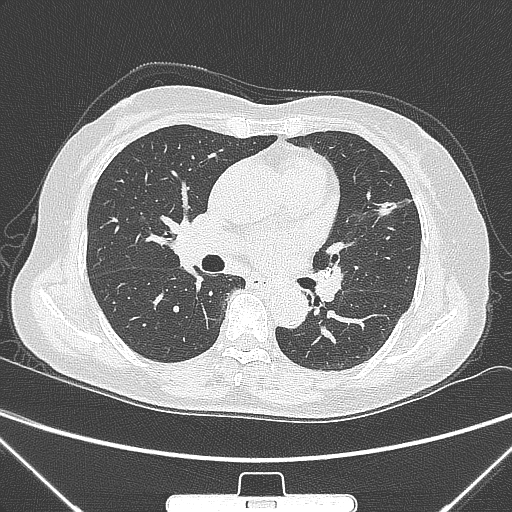
Chest CT, one axial slice; position 151 of 300 along the scan axis; 120 kVp; lung window (W 1500 / L -600 HU); 1 mm slice thickness; 512 × 512 image matrix, field of view 350 × 350 mm. Patient: female, 70 years. Case-level facts recorded for this patient, not image findings: clinical TNM (as recorded): T1b N0 M0; histopathological grade: G2.
Annotated regions visible in this slice (rectangle marked by the reading radiologist):
- lung tumour (recorded histology: adenocarcinoma): box from (x=372, y=193) to (x=406, y=225) px